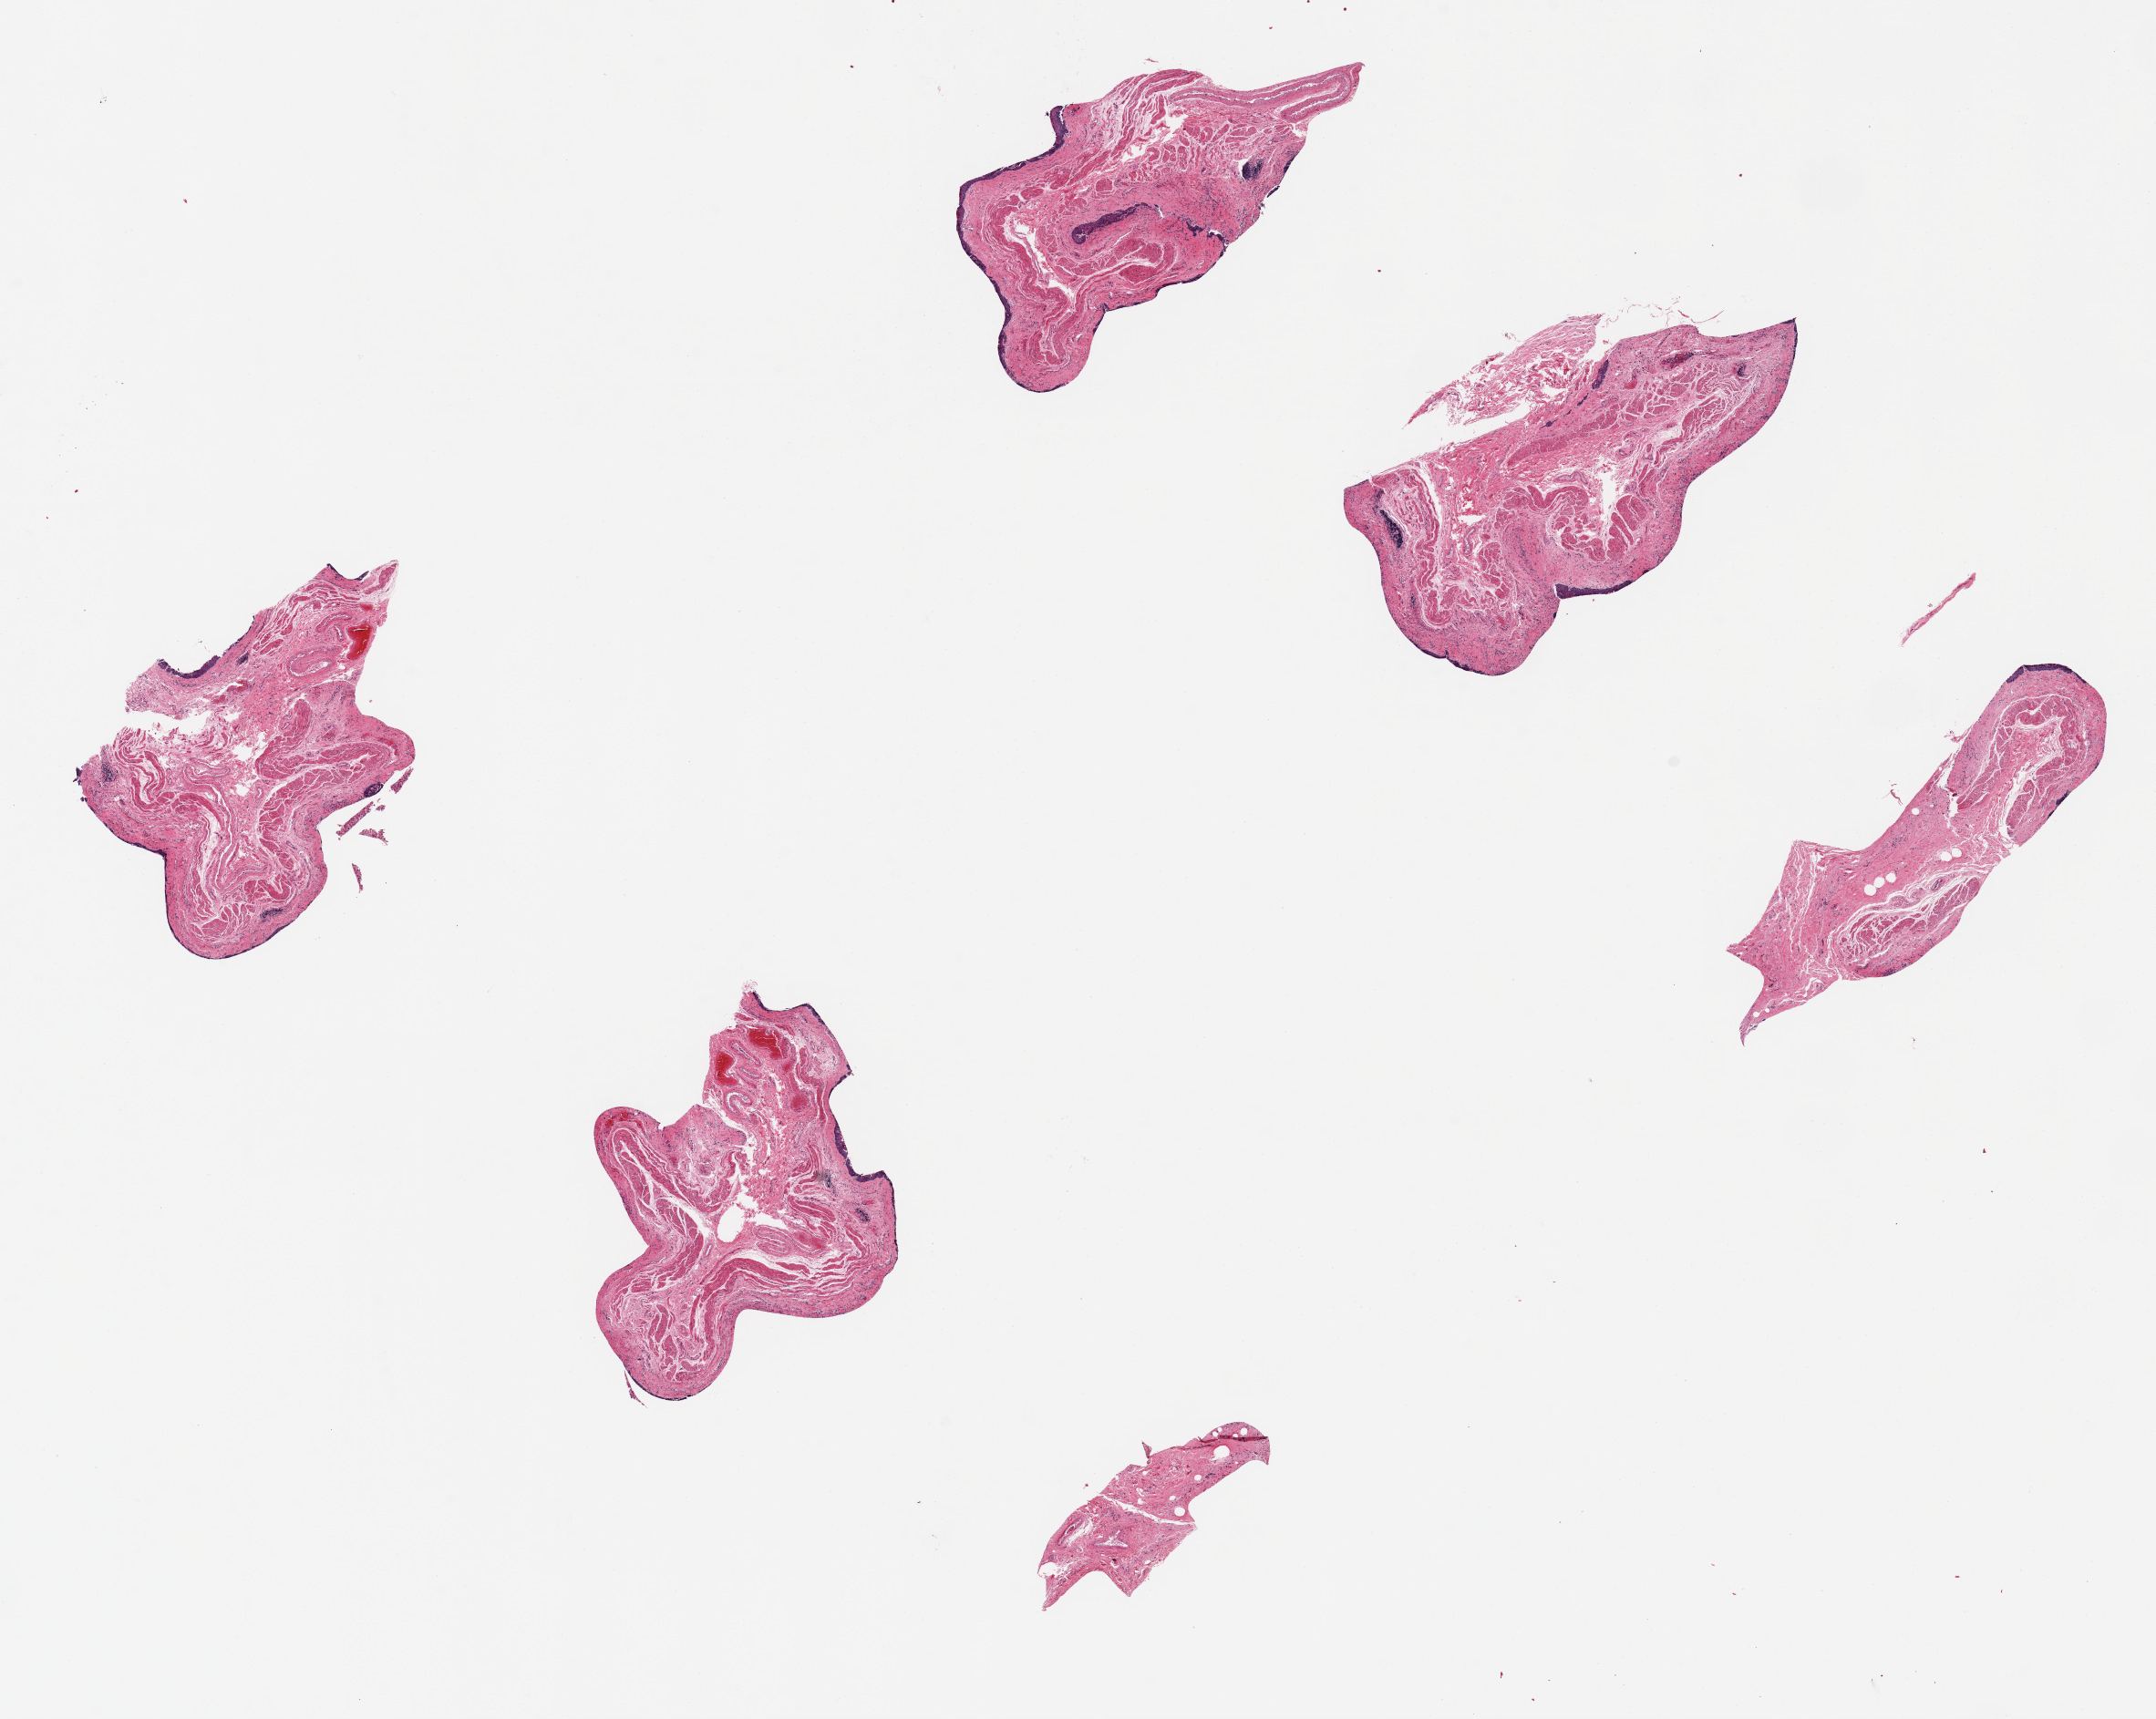
Hematoxylin and eosin (H&E) whole-slide image, brightfield, low-resolution overview of the scanned area, about 18.7 x 14.9 mm (acquisition: 20x scan). PAXgene-fixed paraffin-embedded (PFPE) section. Sampled site (target tissue): esophageal mucous membrane. Tissue donor sample. Male donor.
Review note (as recorded): 6 ~4x2mm pieces, only trace mucosa, less than 5% of thickness.